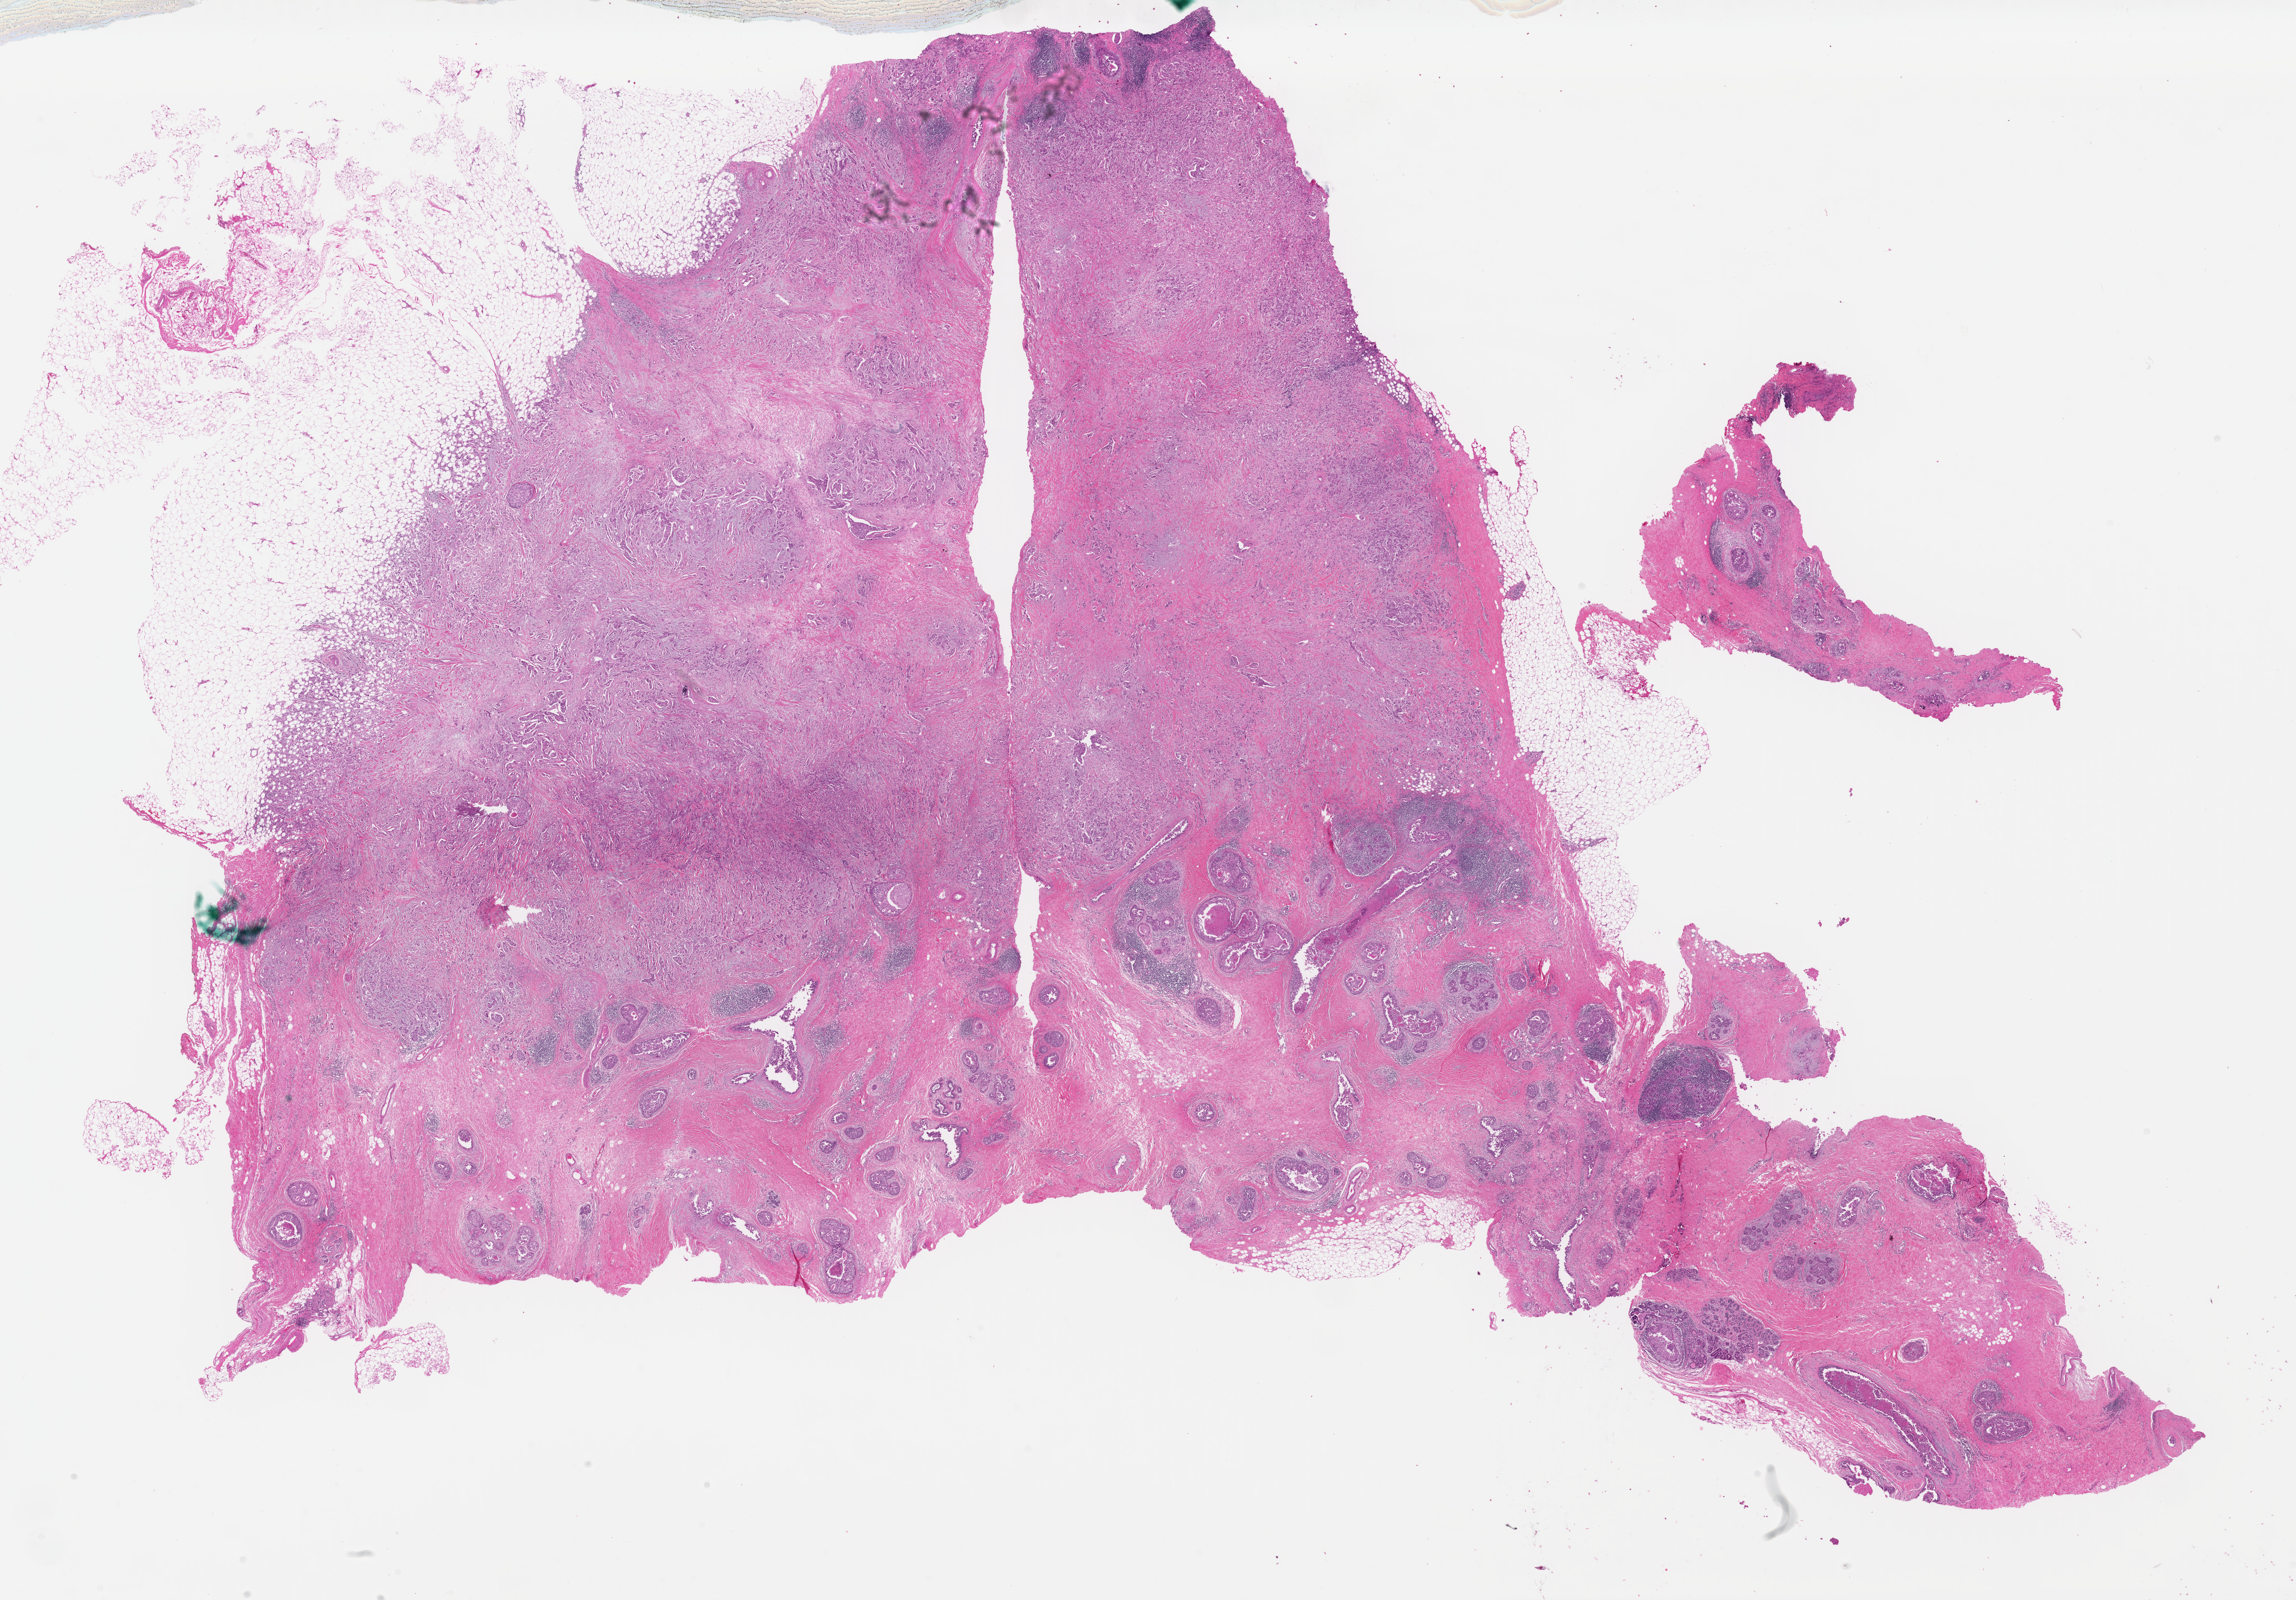
H&E whole-slide image — a low-resolution overview of the entire scanned area, about 31.9 x 22.2 mm (acquisition: 40x scan). FFPE section. Breast, primary tumour sample. Female, age 50 years at initial diagnosis.
Histologic diagnosis: Apocrine adenocarcinoma.